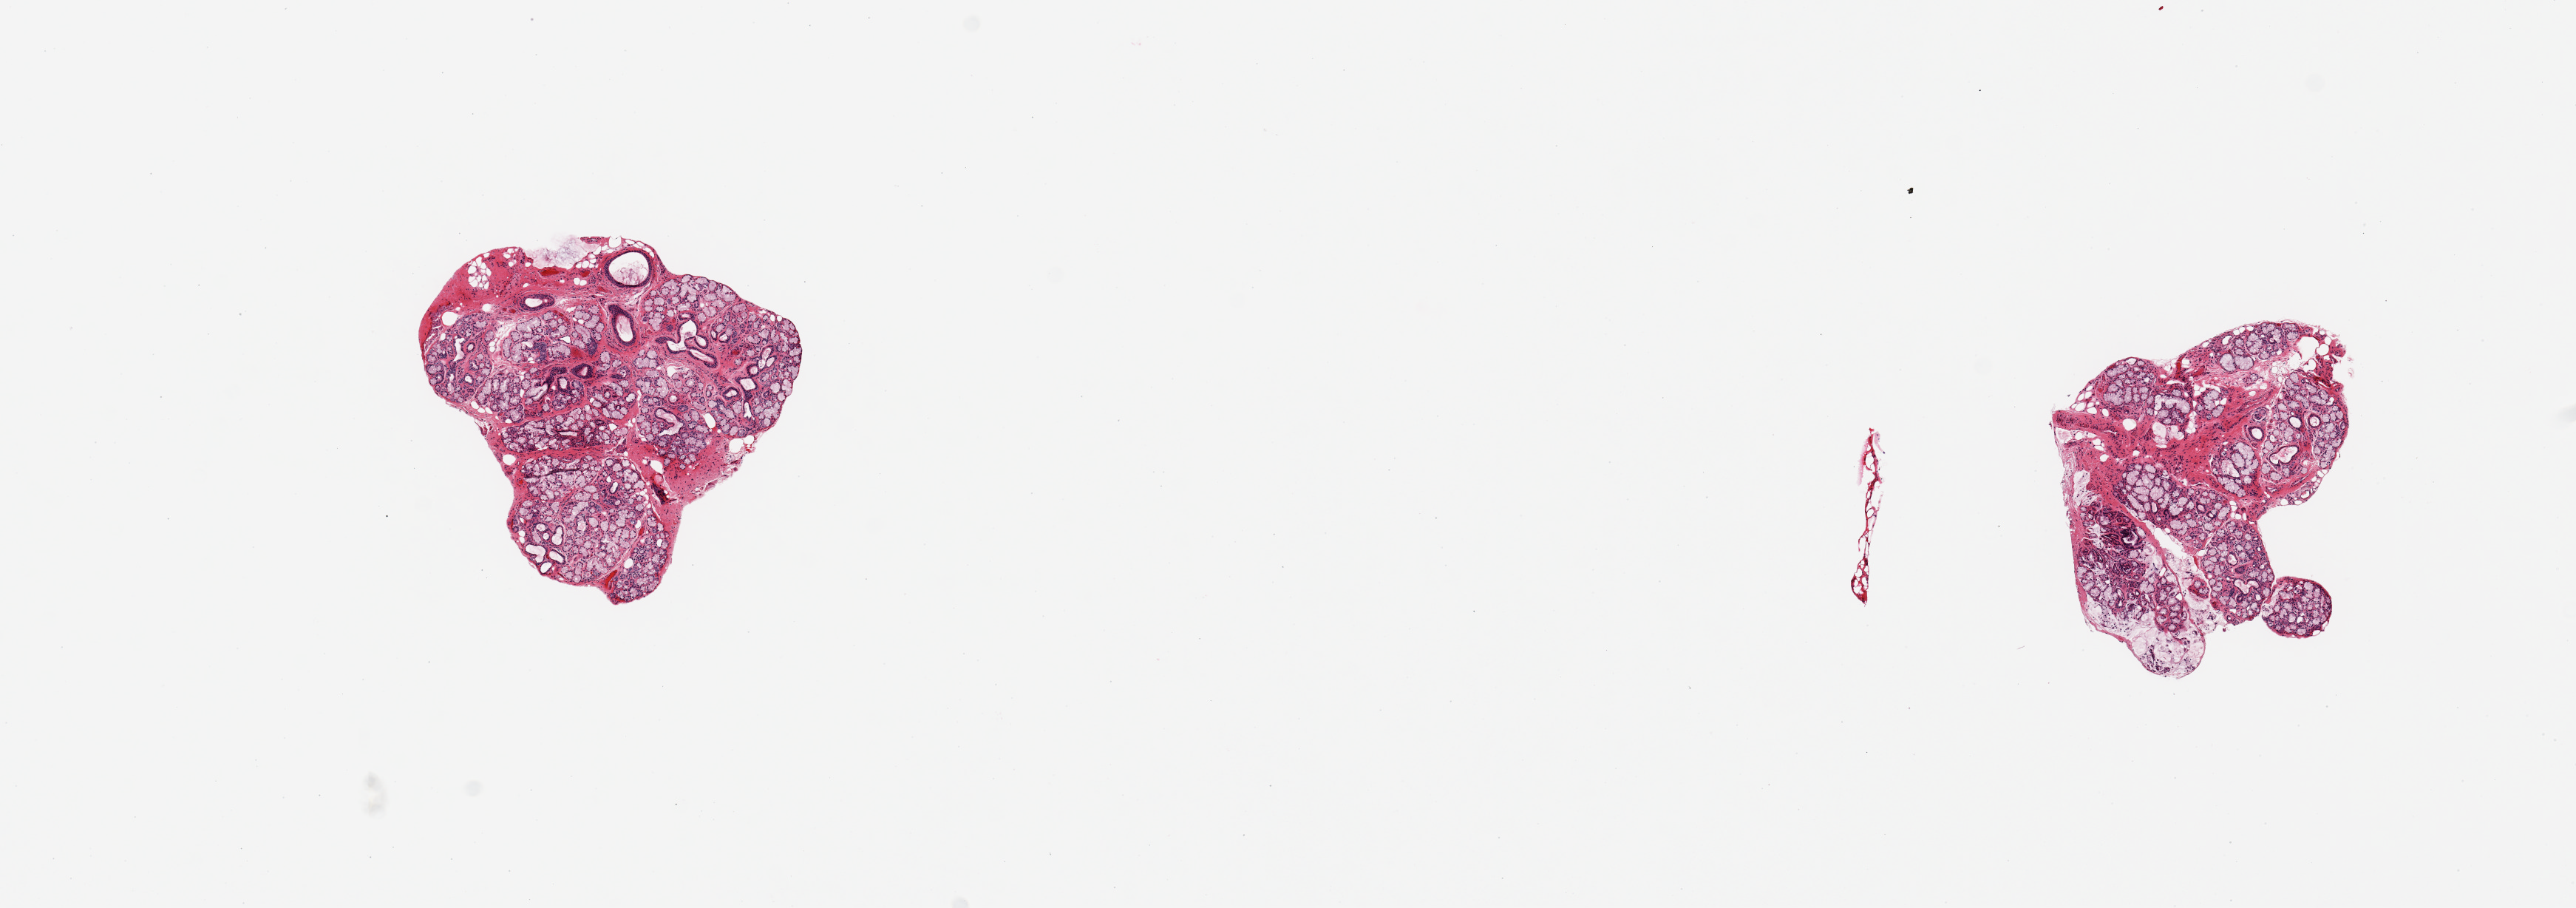
Whole-slide image, H&E stain, brightfield, a low-resolution overview of the entire scanned area, about 13.8 x 4.9 mm (from a 20x scan), PAXgene-fixed paraffin-embedded (PFPE) section, target tissue: minor salivary gland, tissue donor sample.
* reviewer comment on this tissue sample: 2 pieces; well trimmed